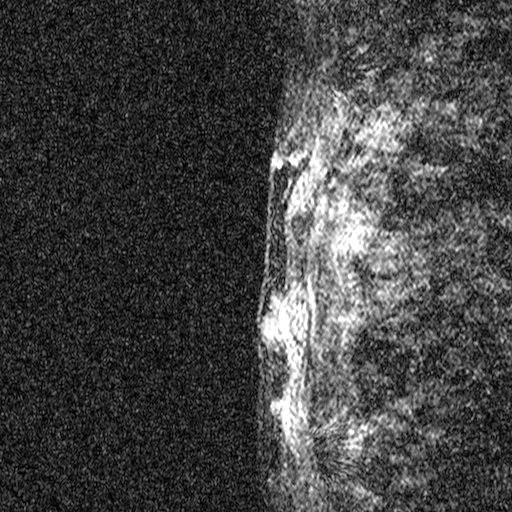
Breast MRI (dynamic contrast-enhanced), one sagittal slice; slice 44 of 44 in the series (ordered by position); dynamic contrast-enhanced study with each time point stored as its own series, time point 2 of 3 at this slice position (early post-contrast, ordered by acquisition time); 1.5 T; TE 4.5 ms, TR 11 ms; 2.05 mm slice thickness; 512 × 512 image matrix, field of view 200 × 200 mm. Female patient, age 44 years. From the clinical record (not read from this slice): setting: breast cancer imaged before/during neoadjuvant chemotherapy; receptor status: HR-positive, HER2-negative.
Structures marked on this image (semi-automatic segmentation, software-assisted and operator-edited):
- analysis volume of interest (the breast-tissue region the enhancement analysis was run in; not a lesion): bounding box [x1, y1, x2, y2] px = [204, 254, 317, 401]
- tumour enhancement mask (voxels above the 90 % enhancement threshold inside the analysis volume of interest): [261, 261, 310, 386]